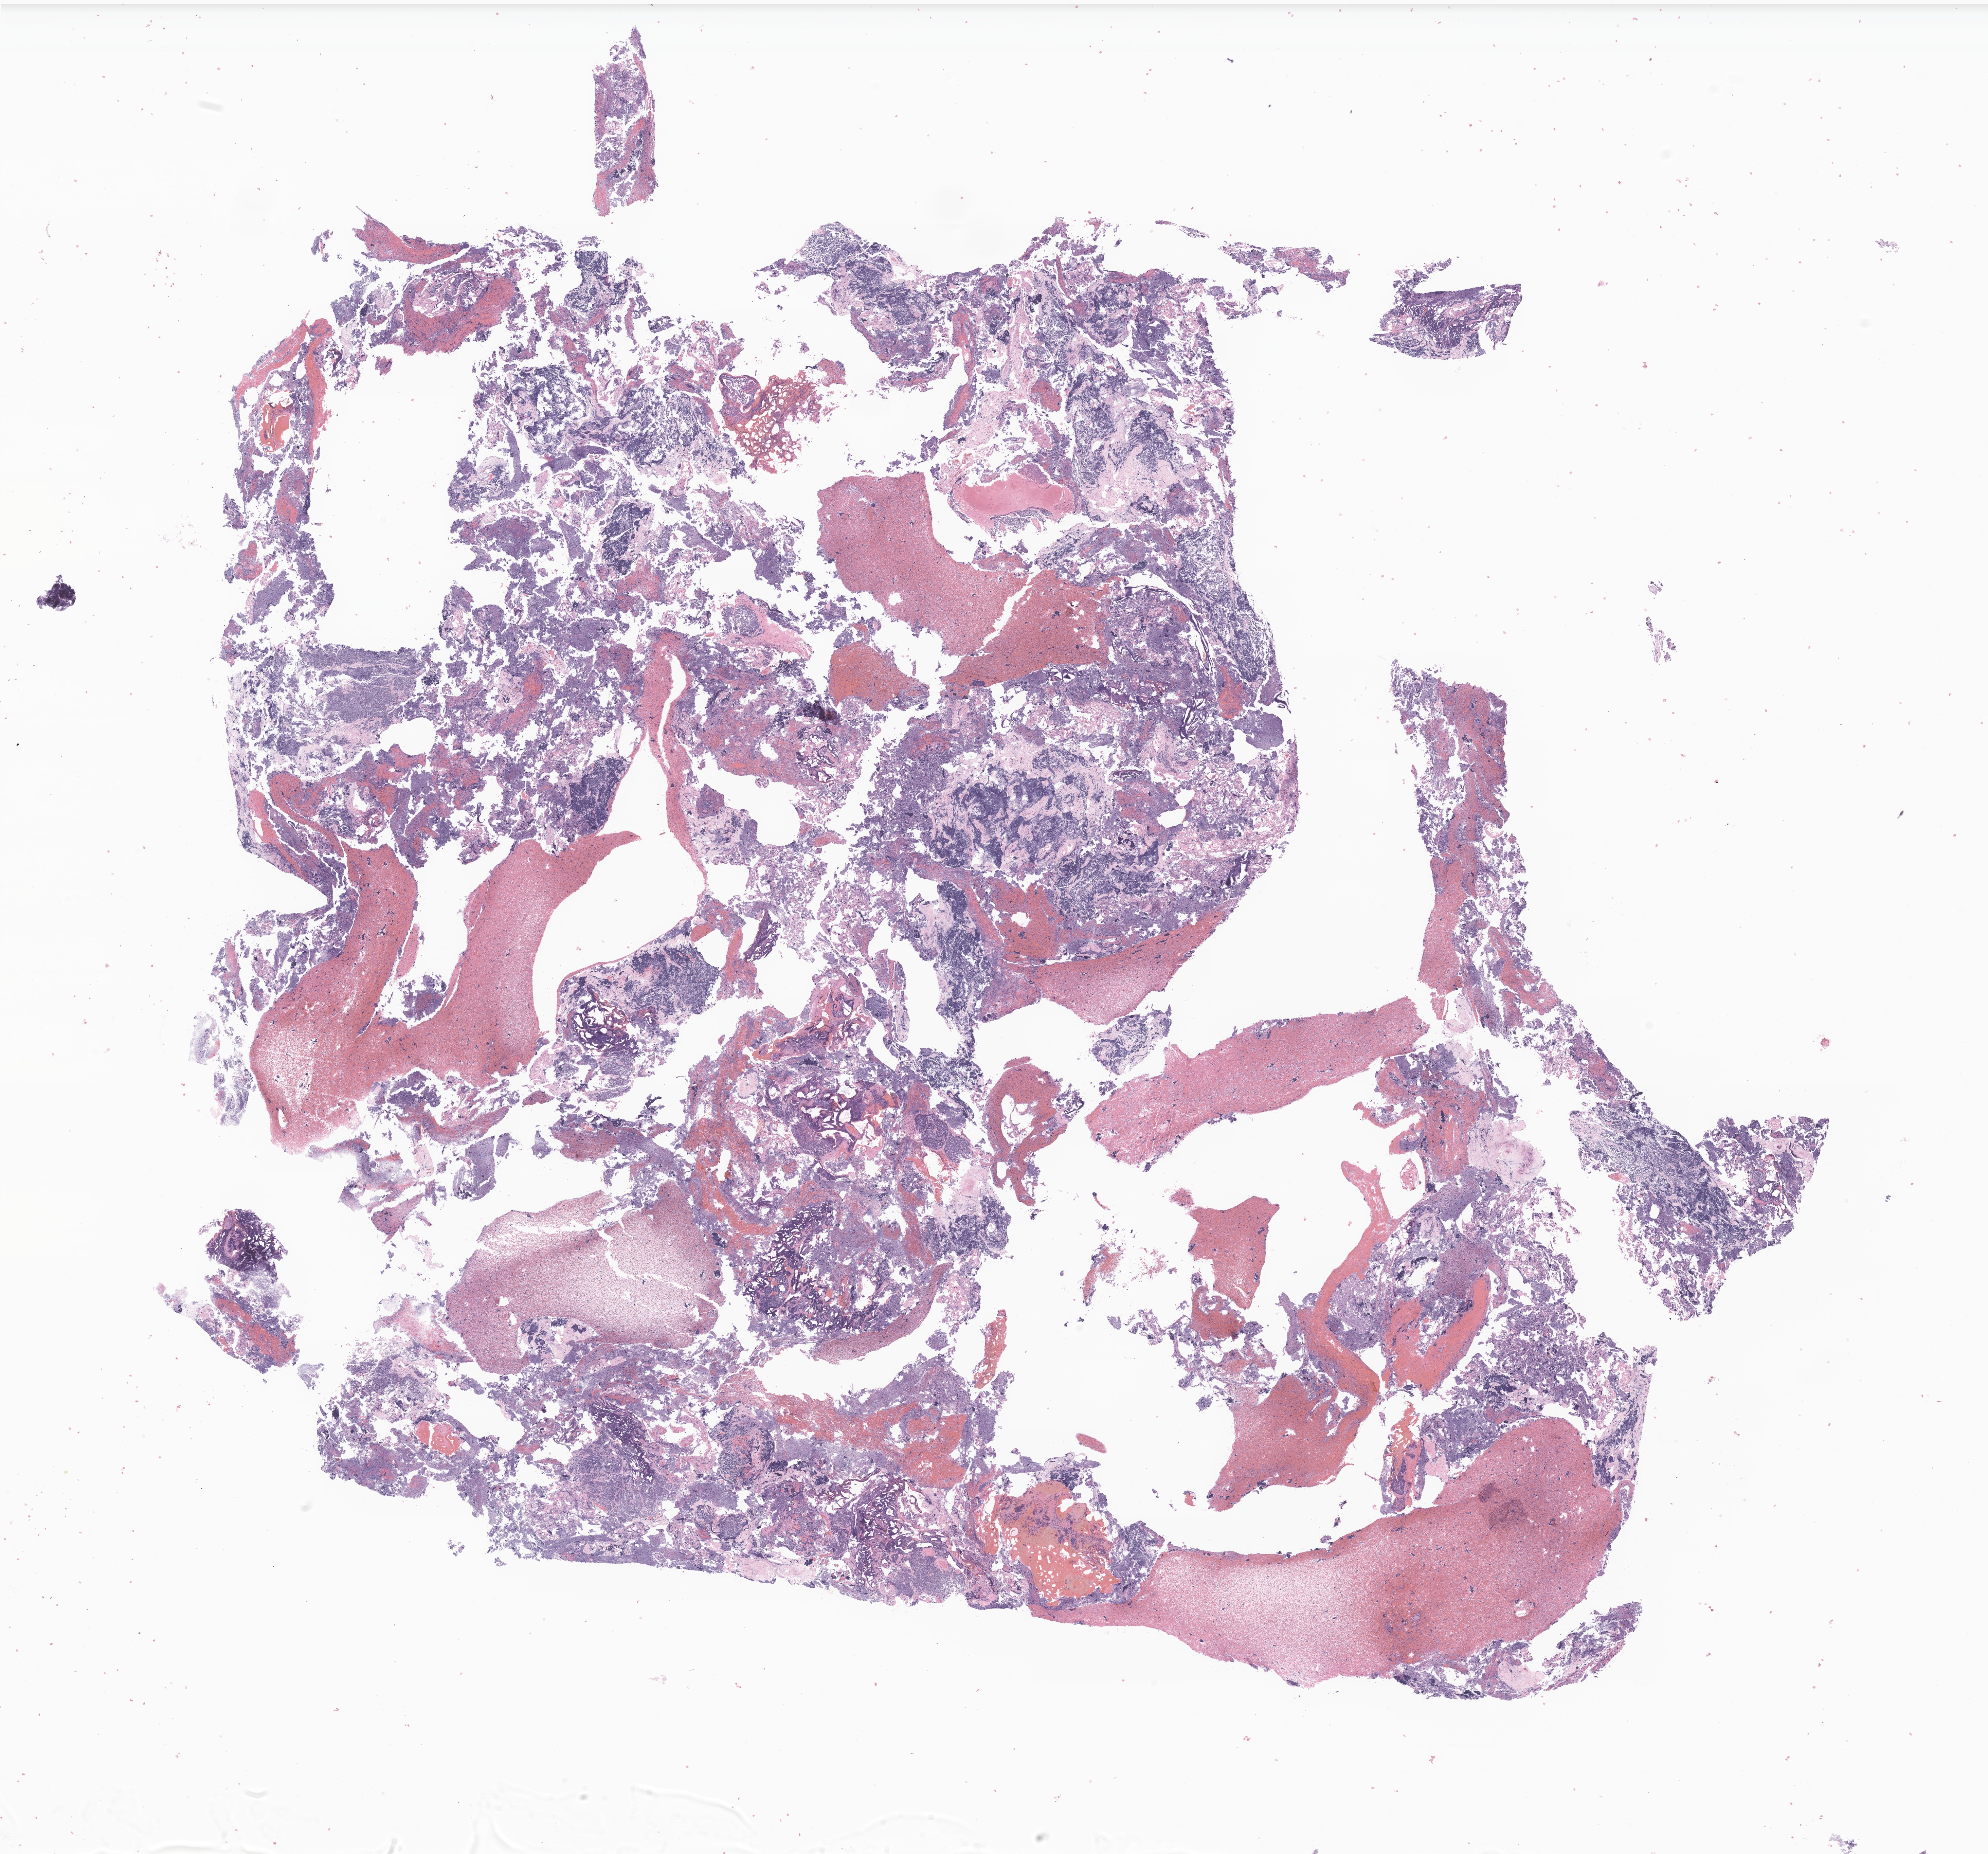
Digitized haematoxylin and eosin-stained section of tumor tissue from the brain, shown as a low-resolution overview of the whole scanned area (about 24.7 x 23.0 mm). FFPE section. Patient male; age 268 months.
• recorded diagnosis: Medulloblastoma, NOS